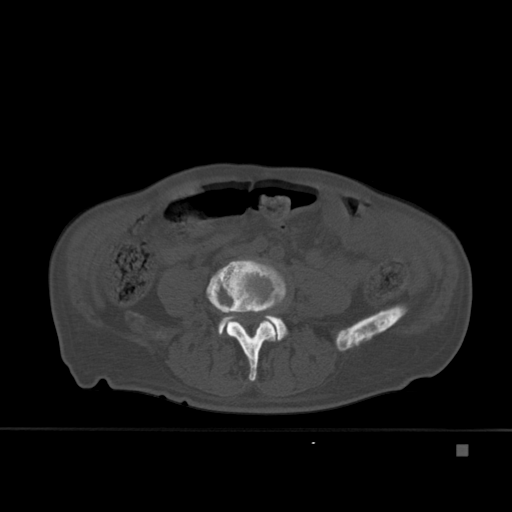
CT including the spine, one axial slice. Position 117 of 451 along the scan axis. Bone window (W 1800 / L 400 HU). 1.5 mm slice thickness. 512 × 512 image matrix, field of view 378 × 378 mm. Patient: male, 75 years. From the clinical record (not read from this slice): primary cancer: prostate.
Structures marked on this image (semi-automatically segmented with operator editing):
- L4 vertebra: bounding box [x1, y1, x2, y2] px = [206, 259, 287, 382]
- L5 vertebra: [219, 316, 288, 341]
- T7 vertebra: [218, 312, 277, 332]